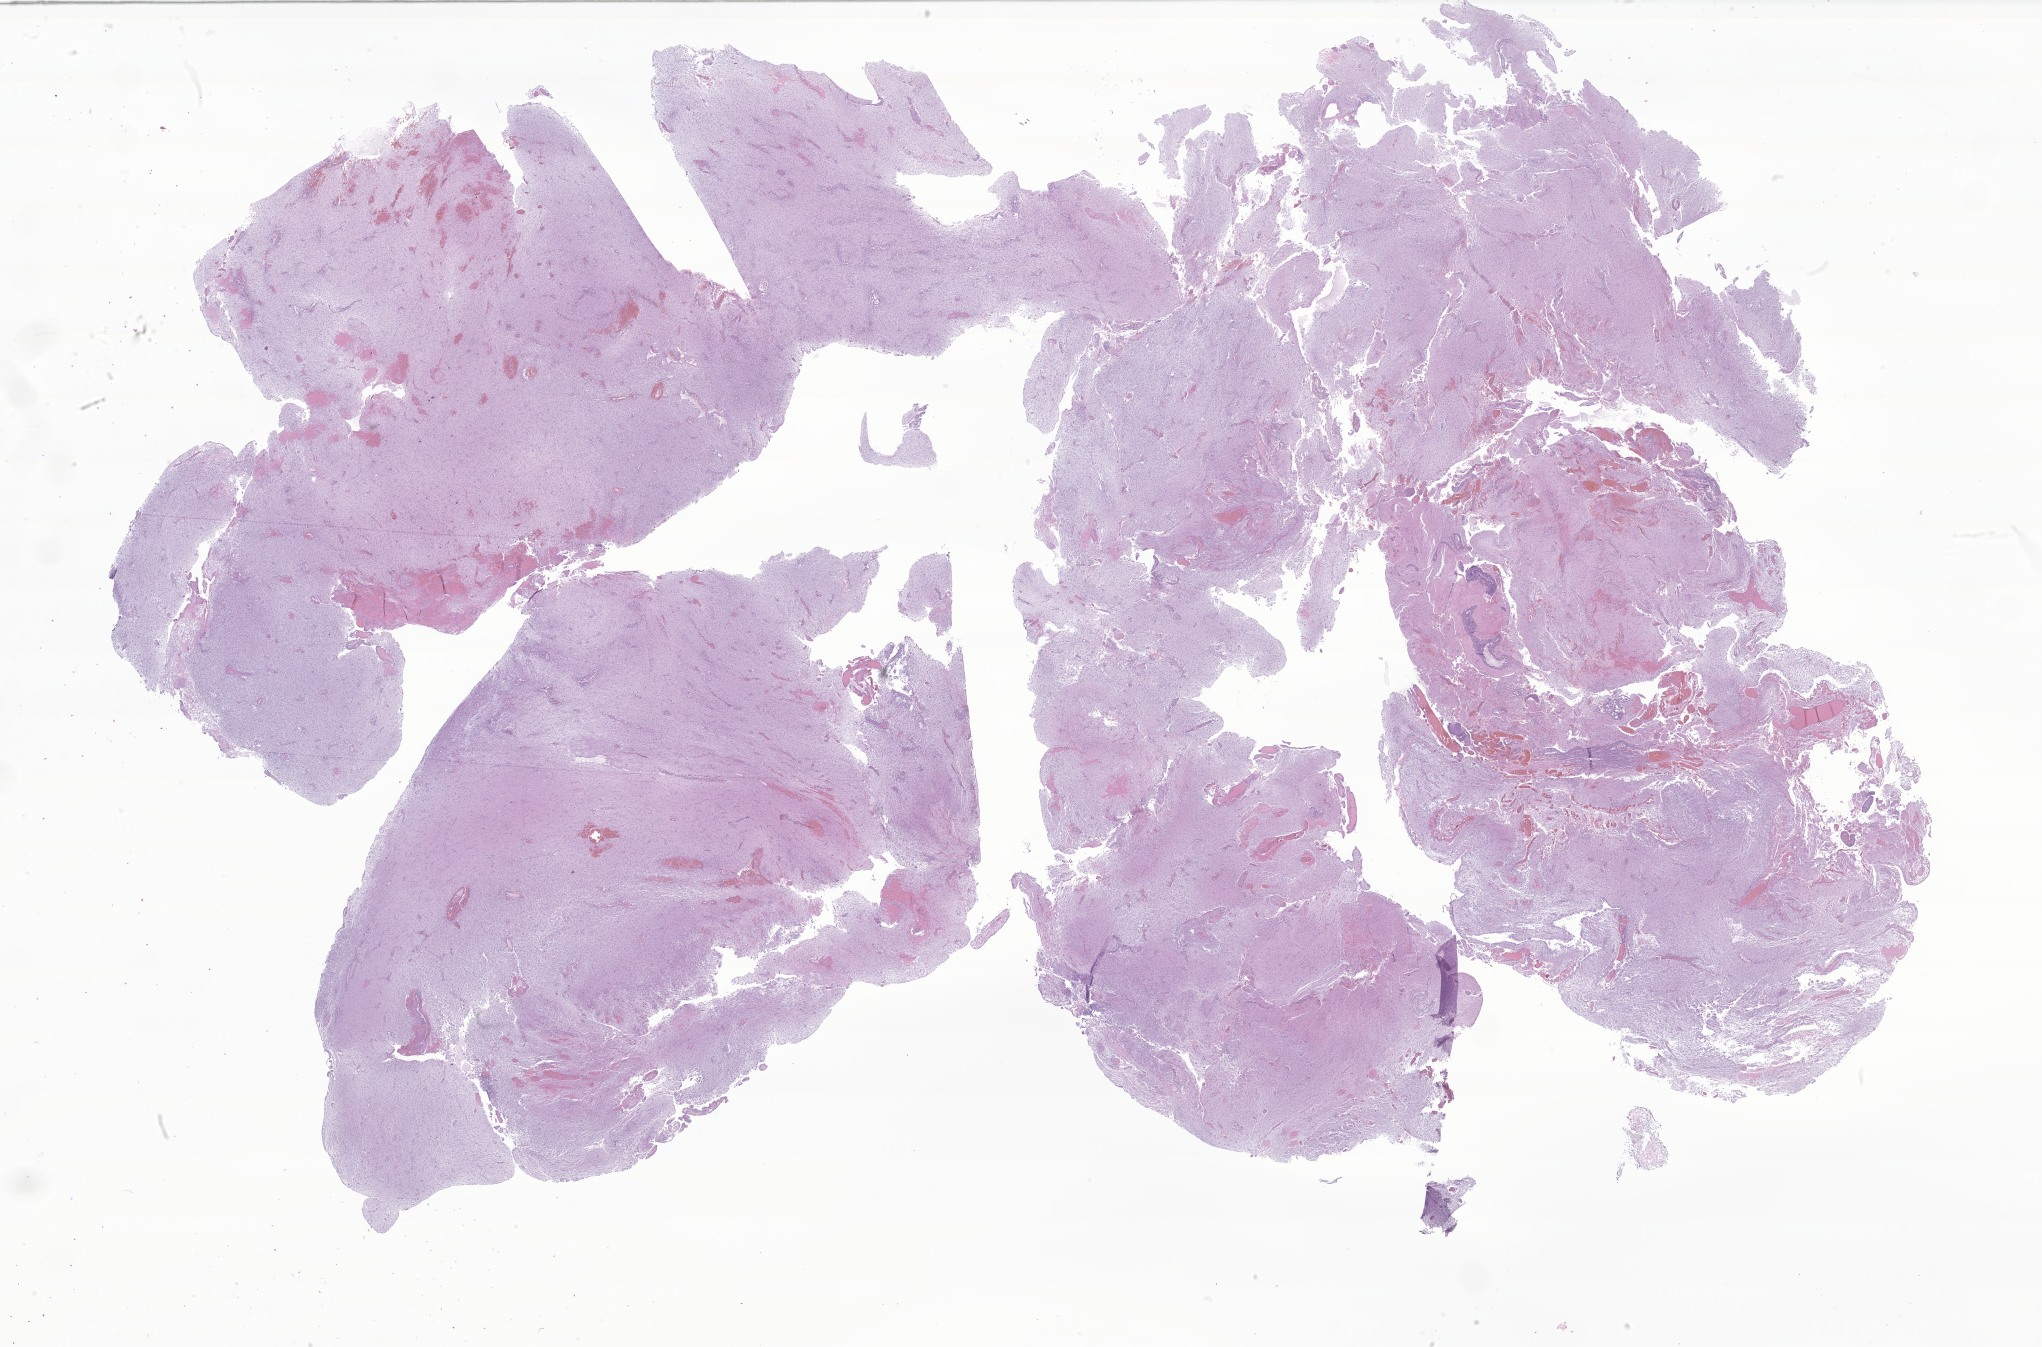
Digitized H&E-stained section of tumor tissue from the cerebellum, a low-resolution overview of the entire scanned area, about 34.4 x 22.7 mm, FFPE section. Male patient, age 44 months (3 years 8 months).
Diagnosis: Pilocytic astrocytoma.